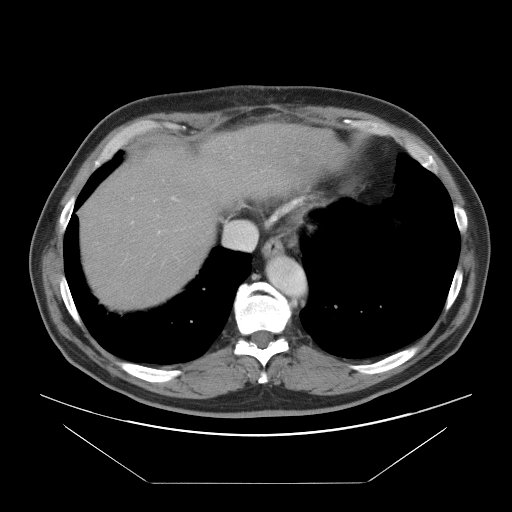
Contrast-enhanced abdominal CT, one axial slice. Position 81 of 97 along the scan axis. Intravenous contrast given. Soft-tissue window (W 400 / L 40 HU). 5 mm slice thickness. 512 × 512 image matrix. Male patient, age 62 years. Case-level facts recorded for this patient, not image findings: diagnosis: colorectal cancer liver metastases, imaged before liver resection; multiple liver metastases: no; largest metastasis: 7 cm; disease in both lobes: yes.
Outlined on this slice (expert manual segmentation):
- hepatic veins: bounding box [x1, y1, x2, y2] px = [223, 221, 257, 250]
- liver: [81, 128, 330, 307]
- planned liver remnant (the part of the liver to remain after resection): [81, 178, 217, 307]
- portal vein (with intrahepatic branches): [131, 197, 176, 234]